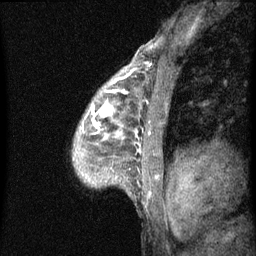
Breast MRI (dynamic contrast-enhanced), one sagittal slice; slice 43 of 60 in the series (ordered by position); dynamic contrast-enhanced series, image 2 of 3 at this slice position (ordered by acquisition); 1.5 T; TE 4.2 ms, TR 8 ms; 256 × 256 image matrix. Patient: female, 50 years.
Annotated regions visible in this slice (semi-automatic segmentation, software-assisted and operator-edited):
- analysis volume of interest (the breast-tissue region the enhancement analysis was run in; not a lesion): bounding box <72,64,141,187> (left, top, right, bottom; pixels)
- tumour enhancement mask (voxels above the 70 % enhancement threshold inside the analysis volume of interest): <82,90,121,135>